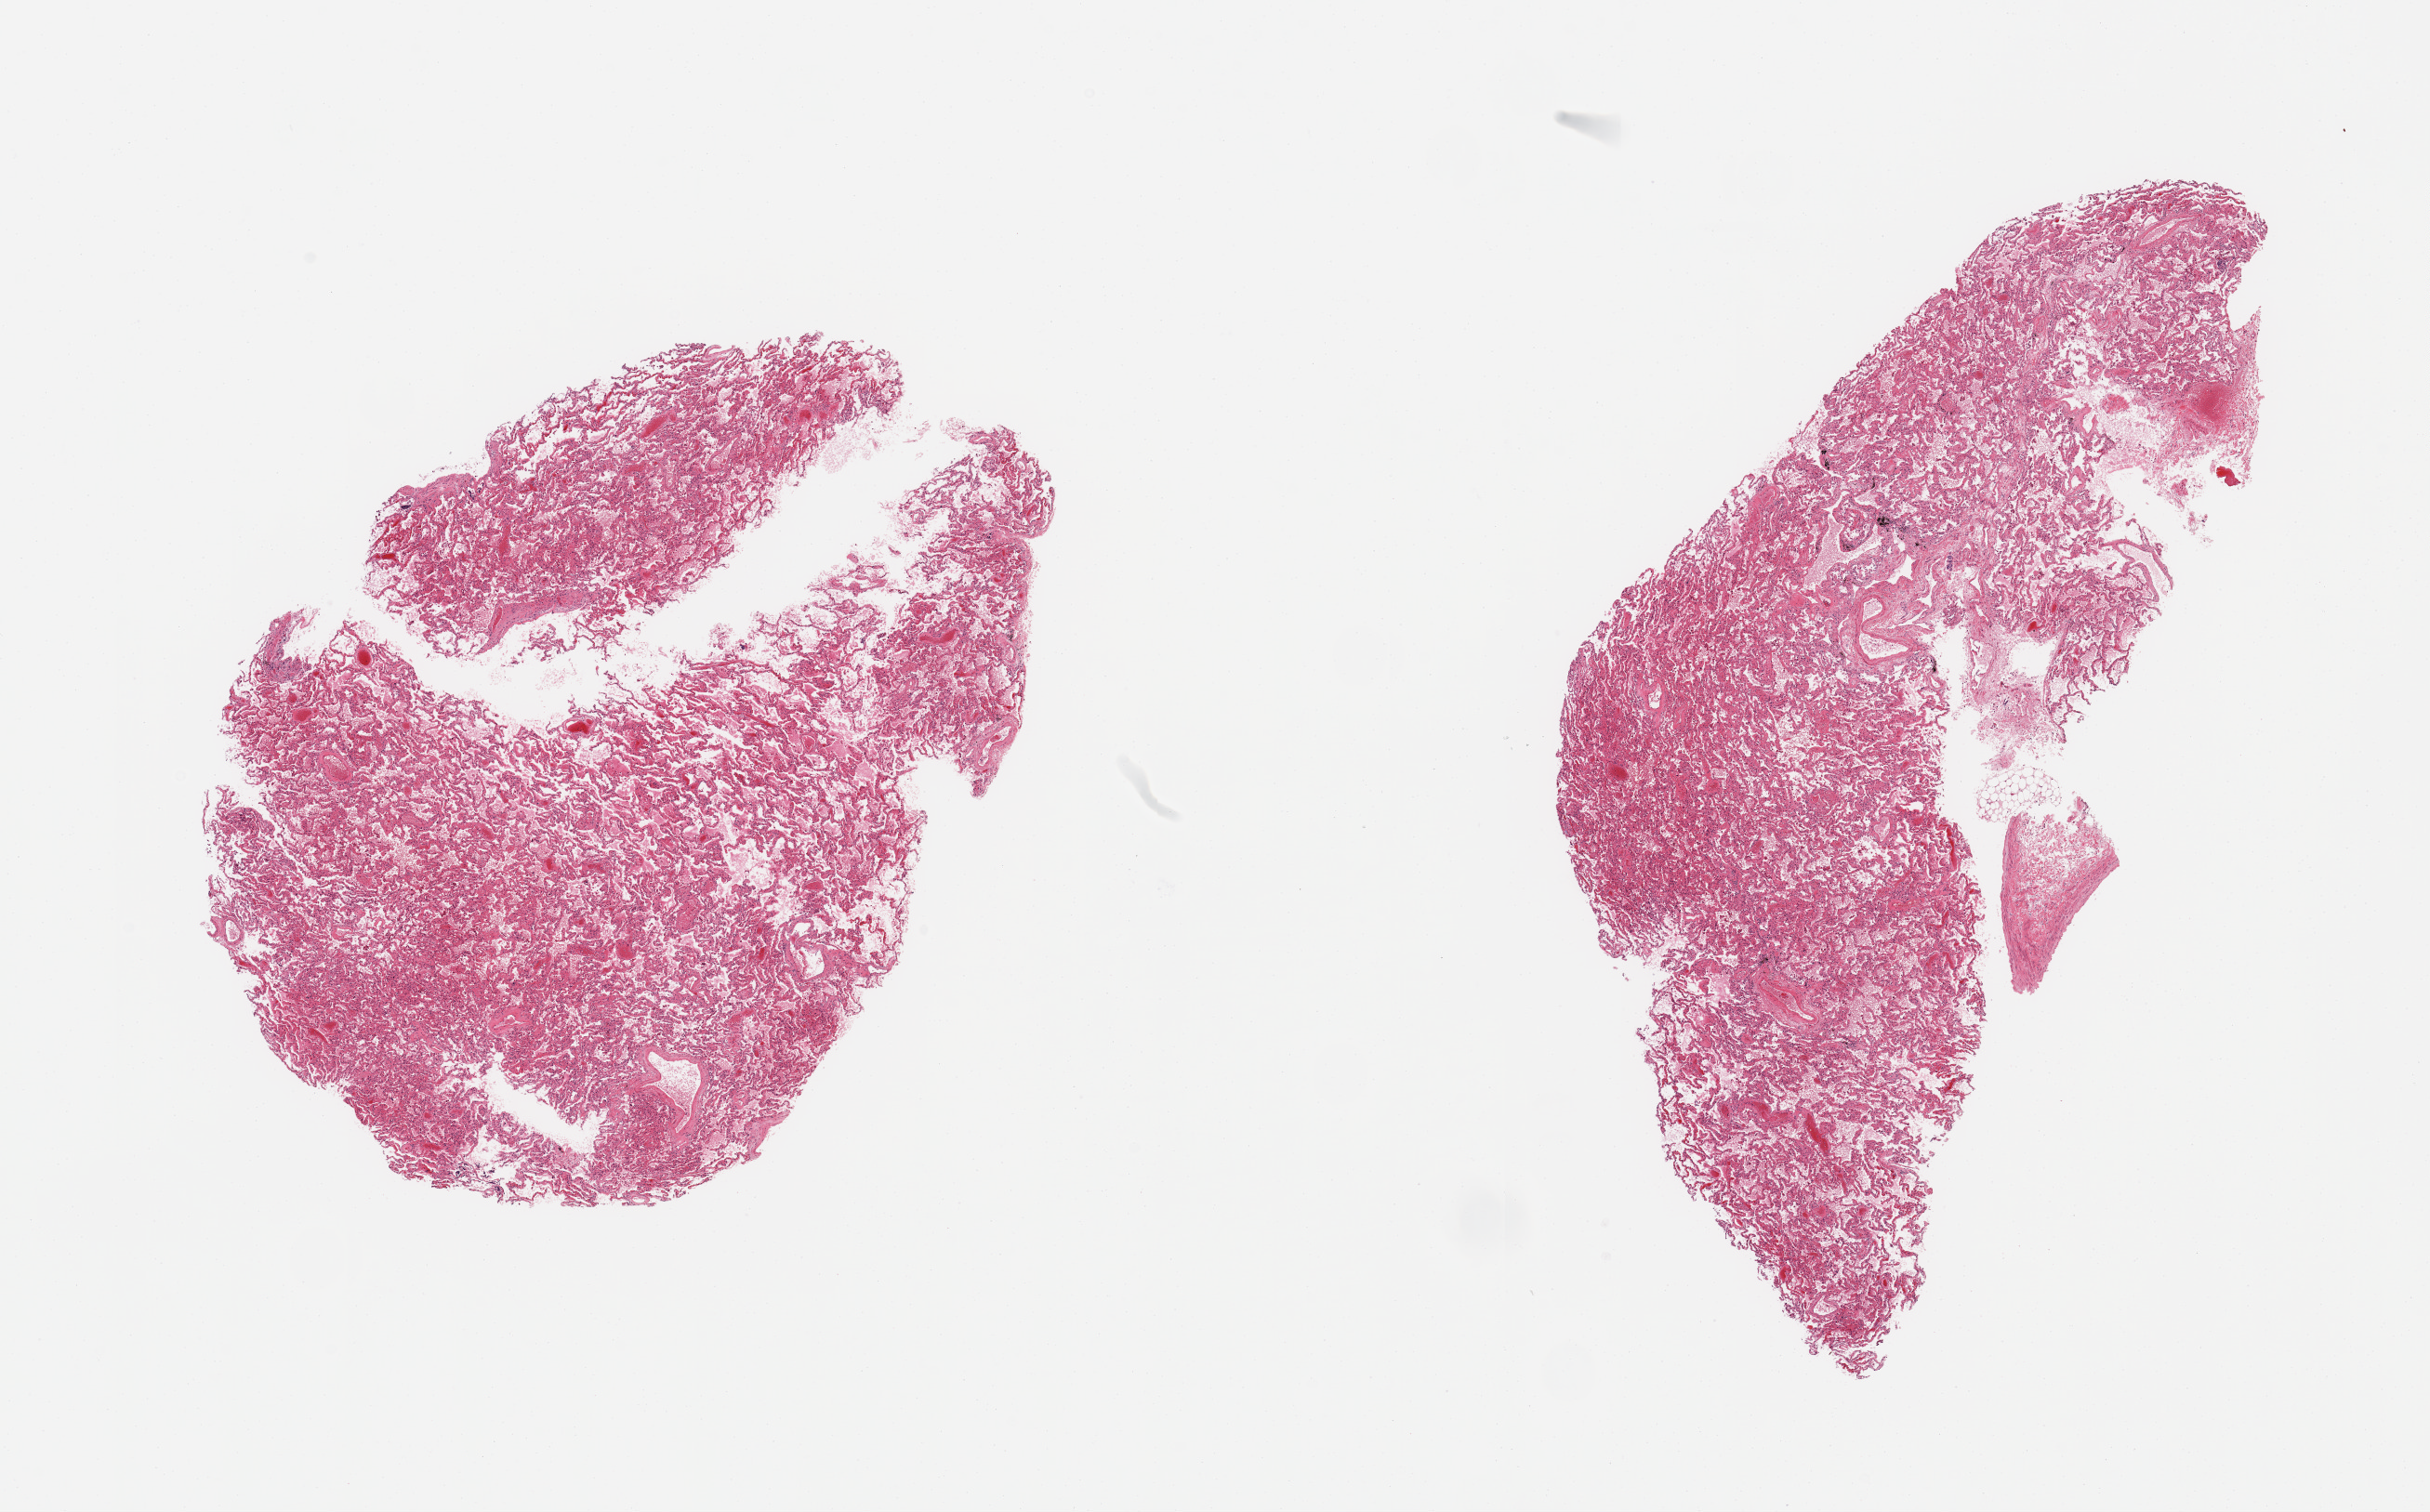
Whole-slide image, haematoxylin and eosin stain, shown as a low-resolution overview of the whole scanned area (about 20.7 x 12.9 mm, acquisition: 20x scan). PAXgene-fixed paraffin-embedded (PFPE) section. Target tissue: lung. Tissue donor sample. Donor sex: male.
Pathologist's review note for this sample: 2 pieces, moderate congestion.